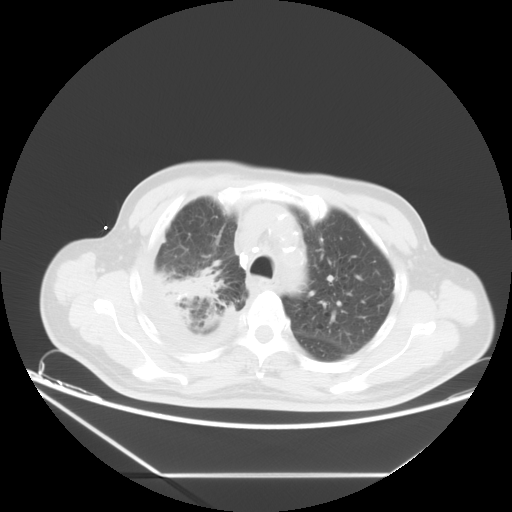
Chest CT, one axial slice. Slice 12 of 20 in the series (ordered by position). 120 kVp. Lung window (W 1500 / L -600 HU). 512 × 512 image matrix, field of view 418 × 418 mm. Patient: male, 75 years. From the clinical record (not read from this slice): clinical TNM (as recorded): T1c N1 M1.
Outlined on this slice (bounding box drawn by a radiologist):
- lung tumour (recorded histology: adenocarcinoma): bounding box <159,269,222,303> (left, top, right, bottom; pixels)